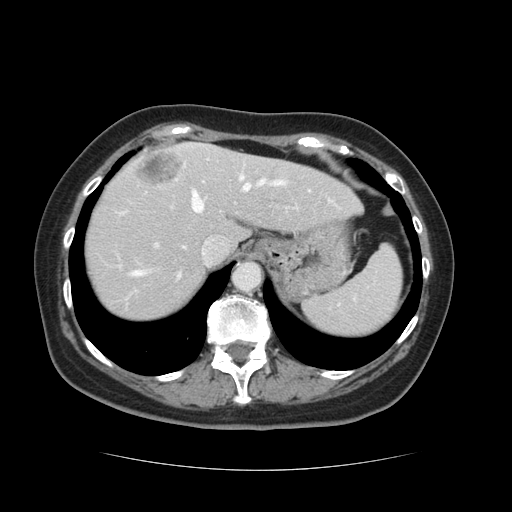
Contrast-enhanced abdominal CT, one axial slice; slice 100 of 128 in the series (ordered by position); 120 kVp; intravenous contrast given; soft-tissue window (W 400 / L 40 HU); 2.5 mm slice thickness; 512 × 512 image matrix, field of view 366 × 366 mm. Female patient, age 67 years. Case-level facts recorded for this patient, not image findings: diagnosis: colorectal cancer liver metastases, imaged before liver resection; multiple liver metastases: yes; largest metastasis: 3 cm; disease in both lobes: yes.
Structures marked on this image (outlined manually by an expert reader):
- hepatic veins: box from (x=128, y=175) to (x=286, y=292) px
- liver: (x=84, y=144)–(x=360, y=323)
- planned liver remnant (the part of the liver to remain after resection): (x=84, y=154)–(x=359, y=322)
- portal vein (with intrahepatic branches): (x=156, y=160)–(x=219, y=246)
- liver metastasis: (x=136, y=151)–(x=186, y=184)